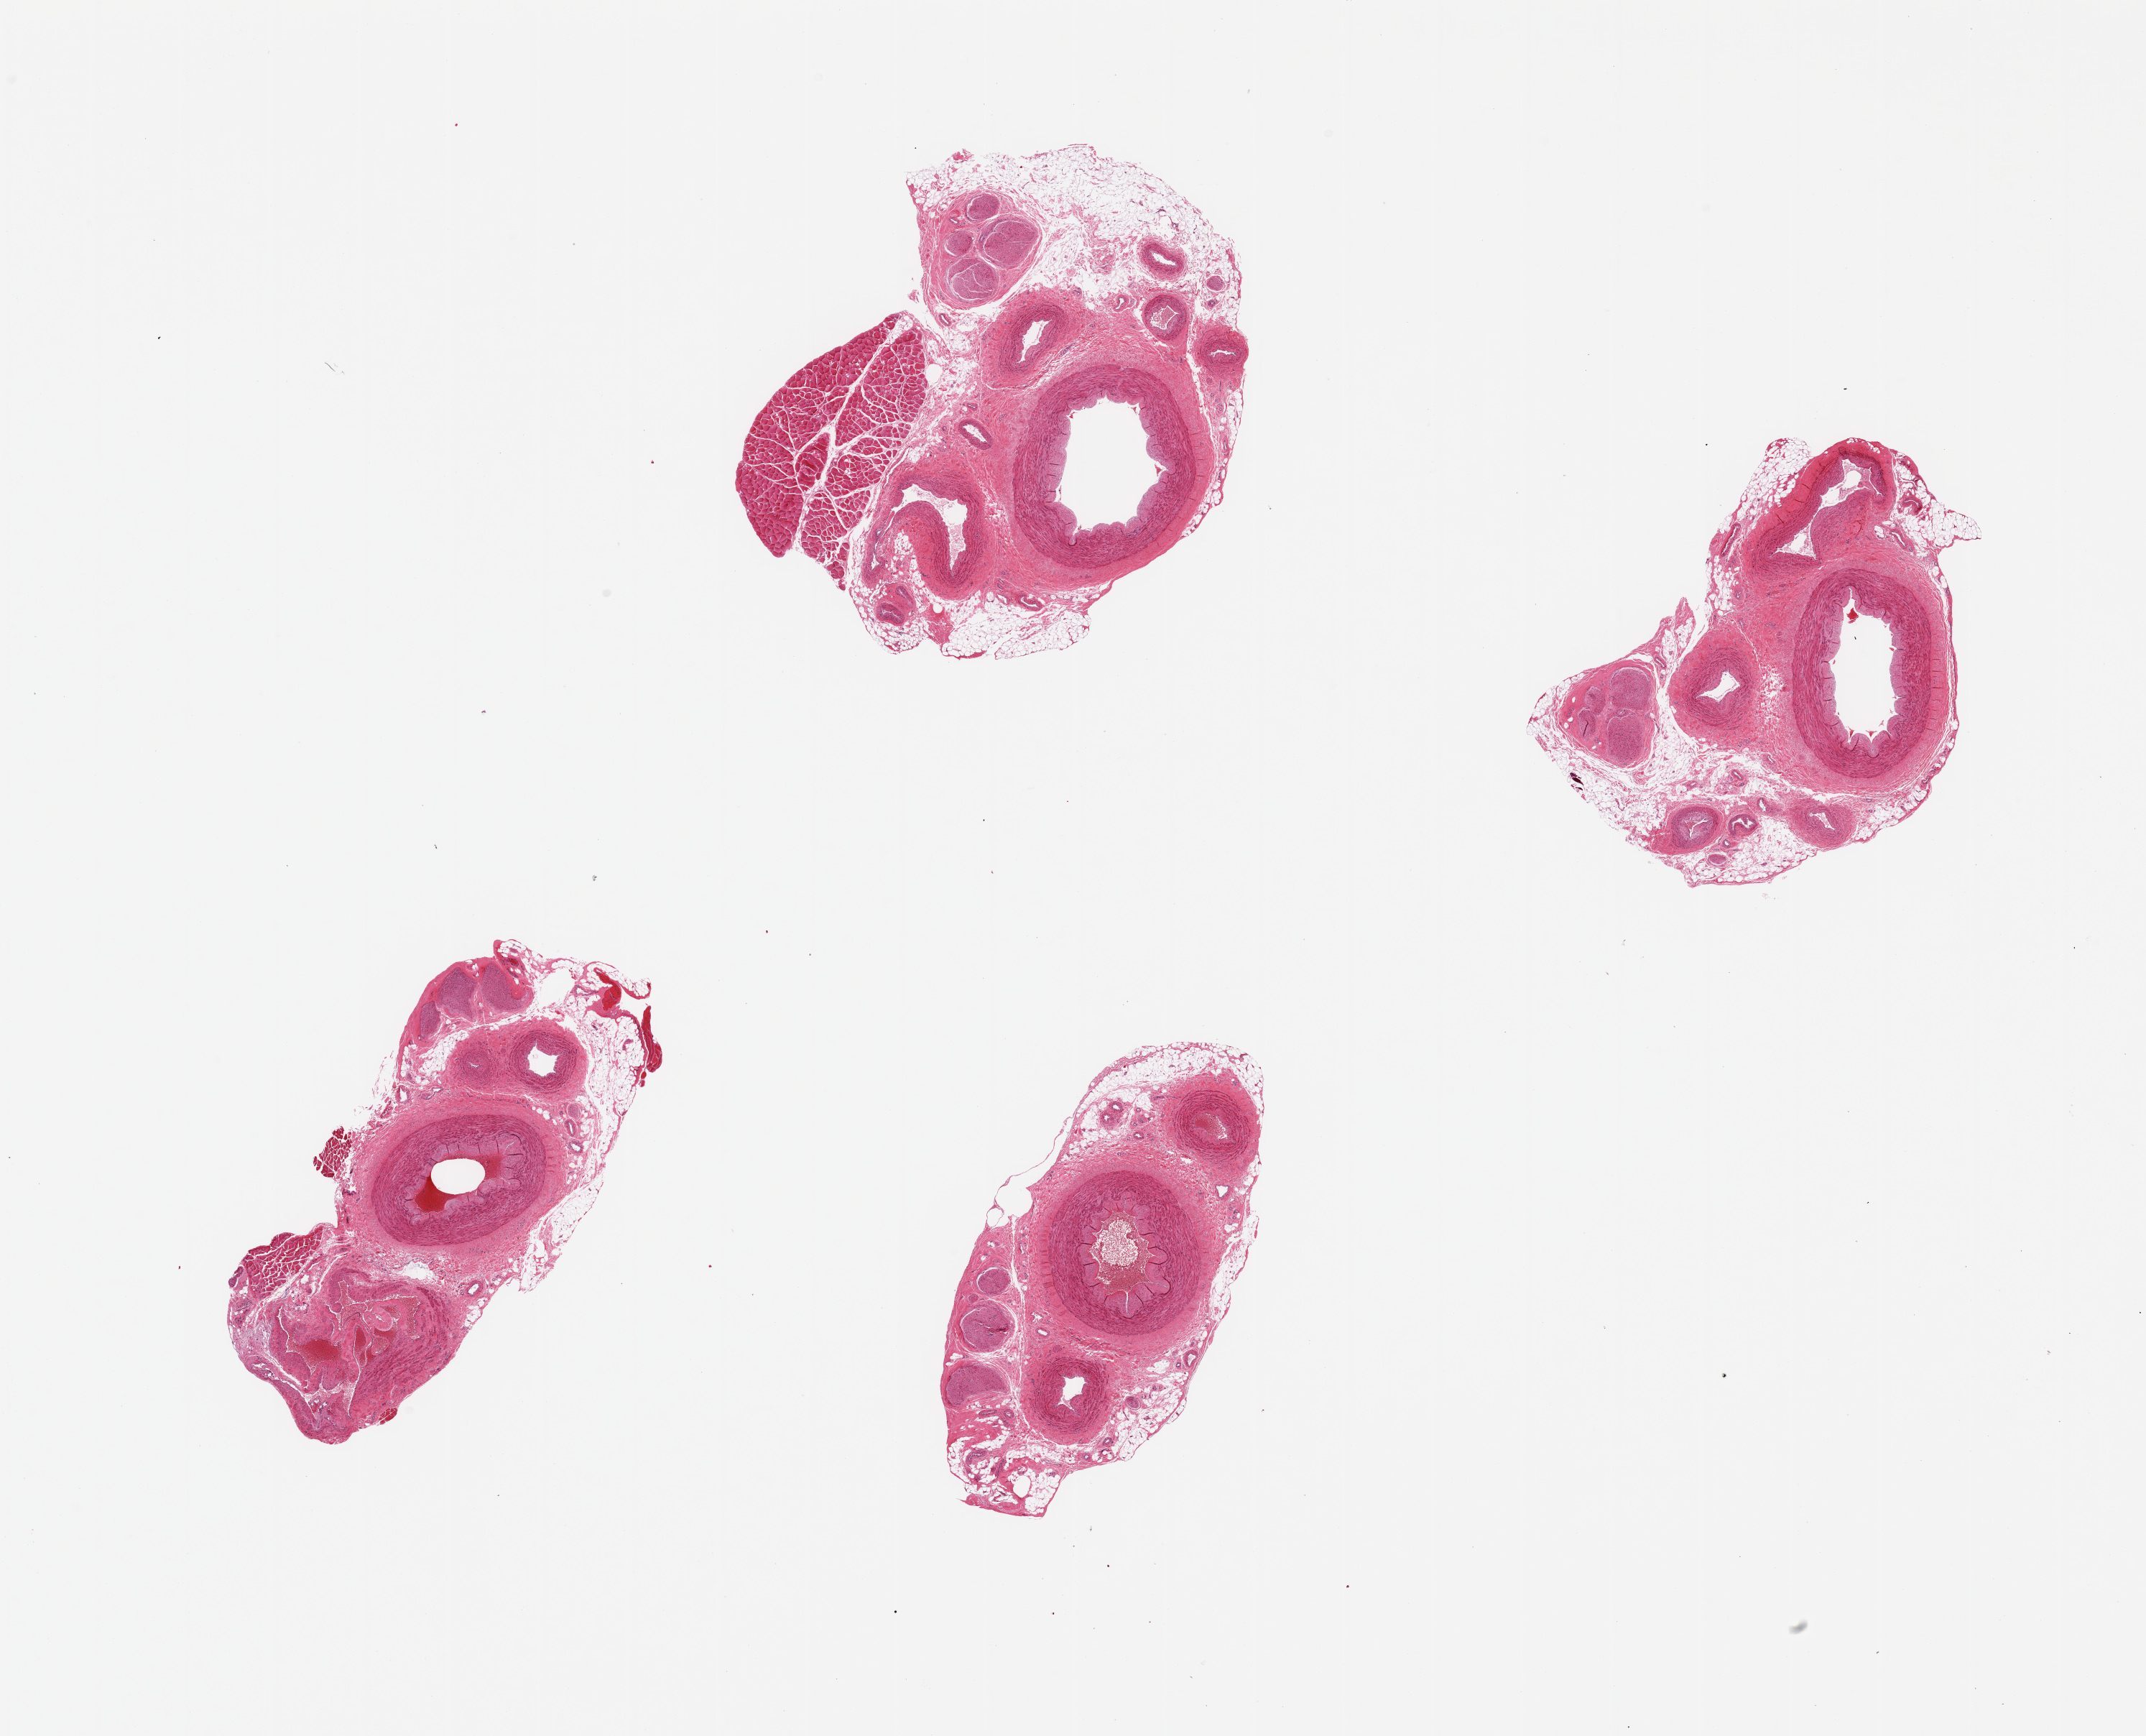
Whole-slide image, hematoxylin and eosin (H&E) stain — shown as a low-resolution overview of the whole scanned area (about 23.6 x 19.1 mm, acquisition: 20x scan). PAXgene-fixed paraffin-embedded (PFPE) section. Section of tibial artery (target tissue). Tissue donor sample. Donor sex: male.
Review note (as recorded): 4 pieces; multiple cross sections of small vessels with attached fibroadipose tissue and nerves and skeletal muscle; boxed calcification.